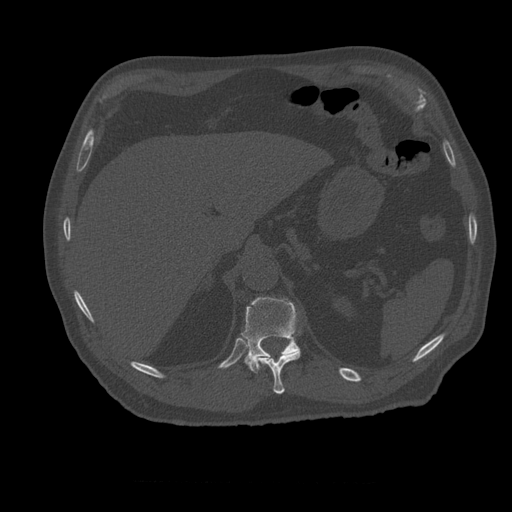
CT including the spine, one axial slice. Slice 270 of 399 in the series (ordered by position). Bone window (W 1800 / L 400 HU). 1.25 mm slice thickness. 512 × 512 image matrix. Patient age 73 years. Case-level facts recorded for this patient, not image findings: primary cancer: prostate; vertebrae with lytic lesions (as recorded): L2.
Structures marked on this image (semi-automatic segmentation, software-assisted and operator-edited):
- T11 vertebra: bounding box (x1, y1, x2, y2) in pixels: (257, 352, 301, 394)
- T12 vertebra: (241, 297, 301, 373)